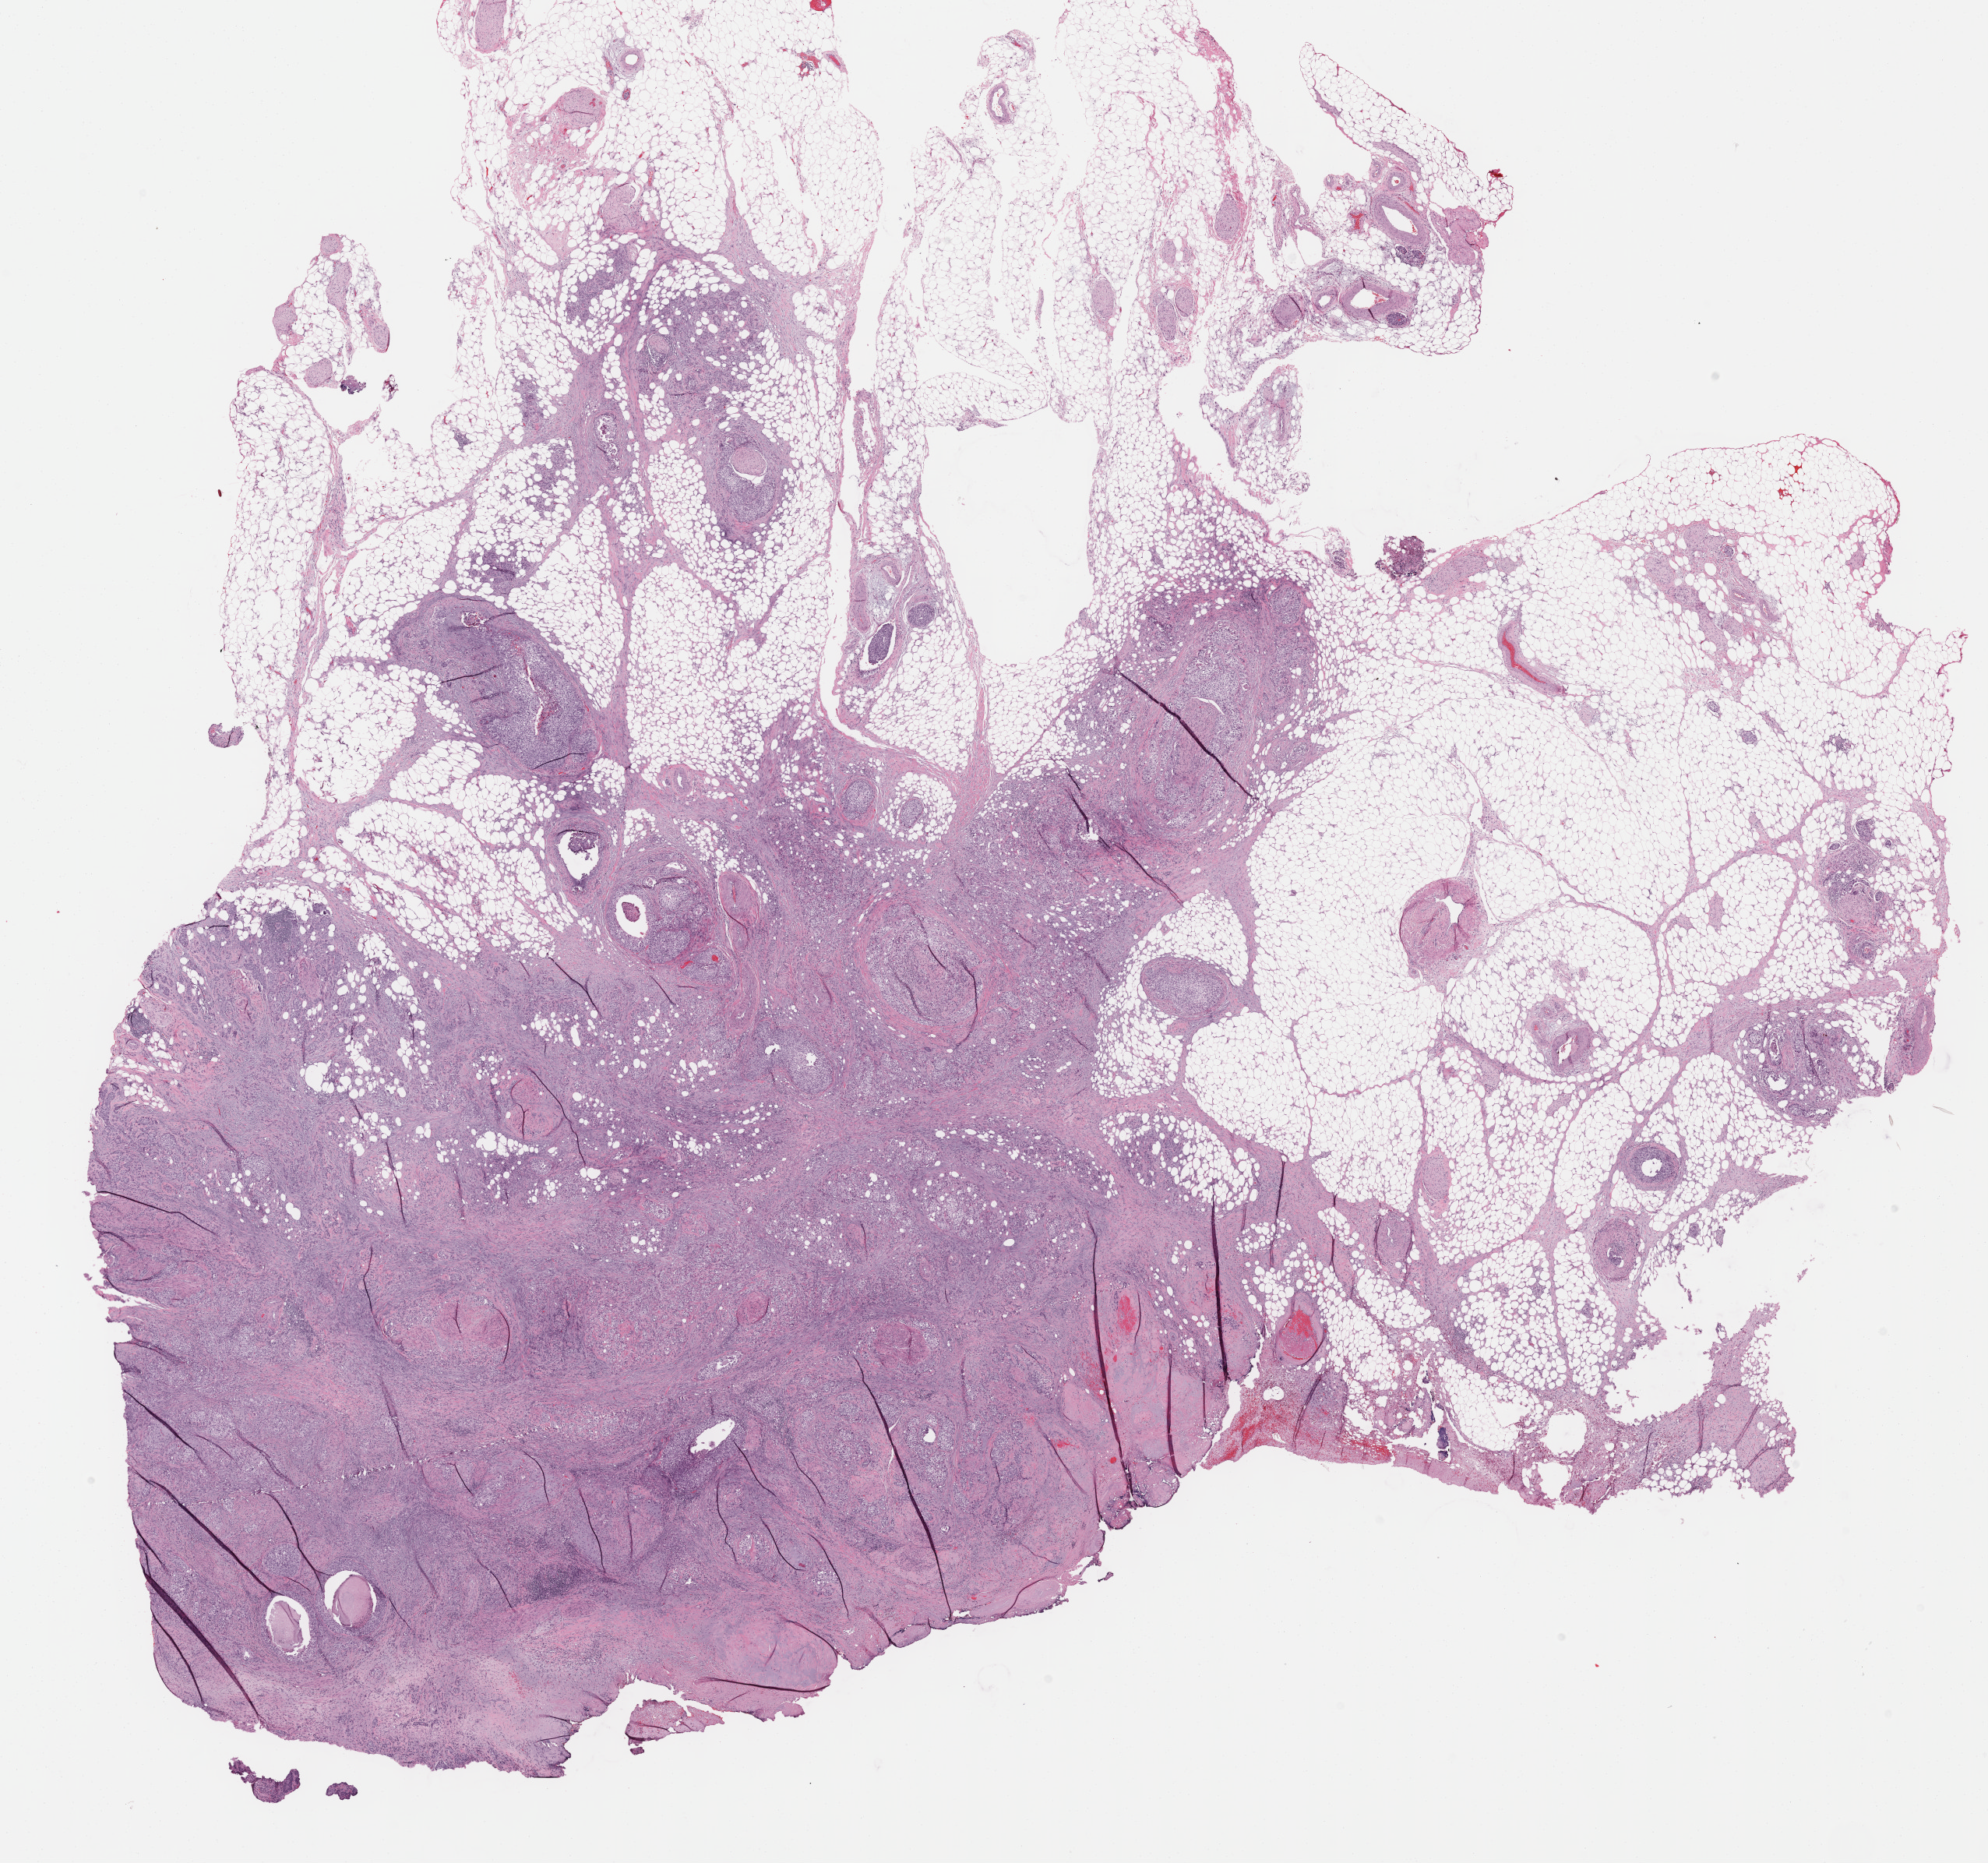
H&E whole-slide image, low-resolution overview of the scanned area, about 20.6 x 19.3 mm. Formalin-fixed paraffin-embedded (FFPE) diagnostic section. Bladder, primary tumour sample. Patient: male, age at initial diagnosis 87 years.
Histologic diagnosis: Transitional cell carcinoma (lateral wall of bladder).